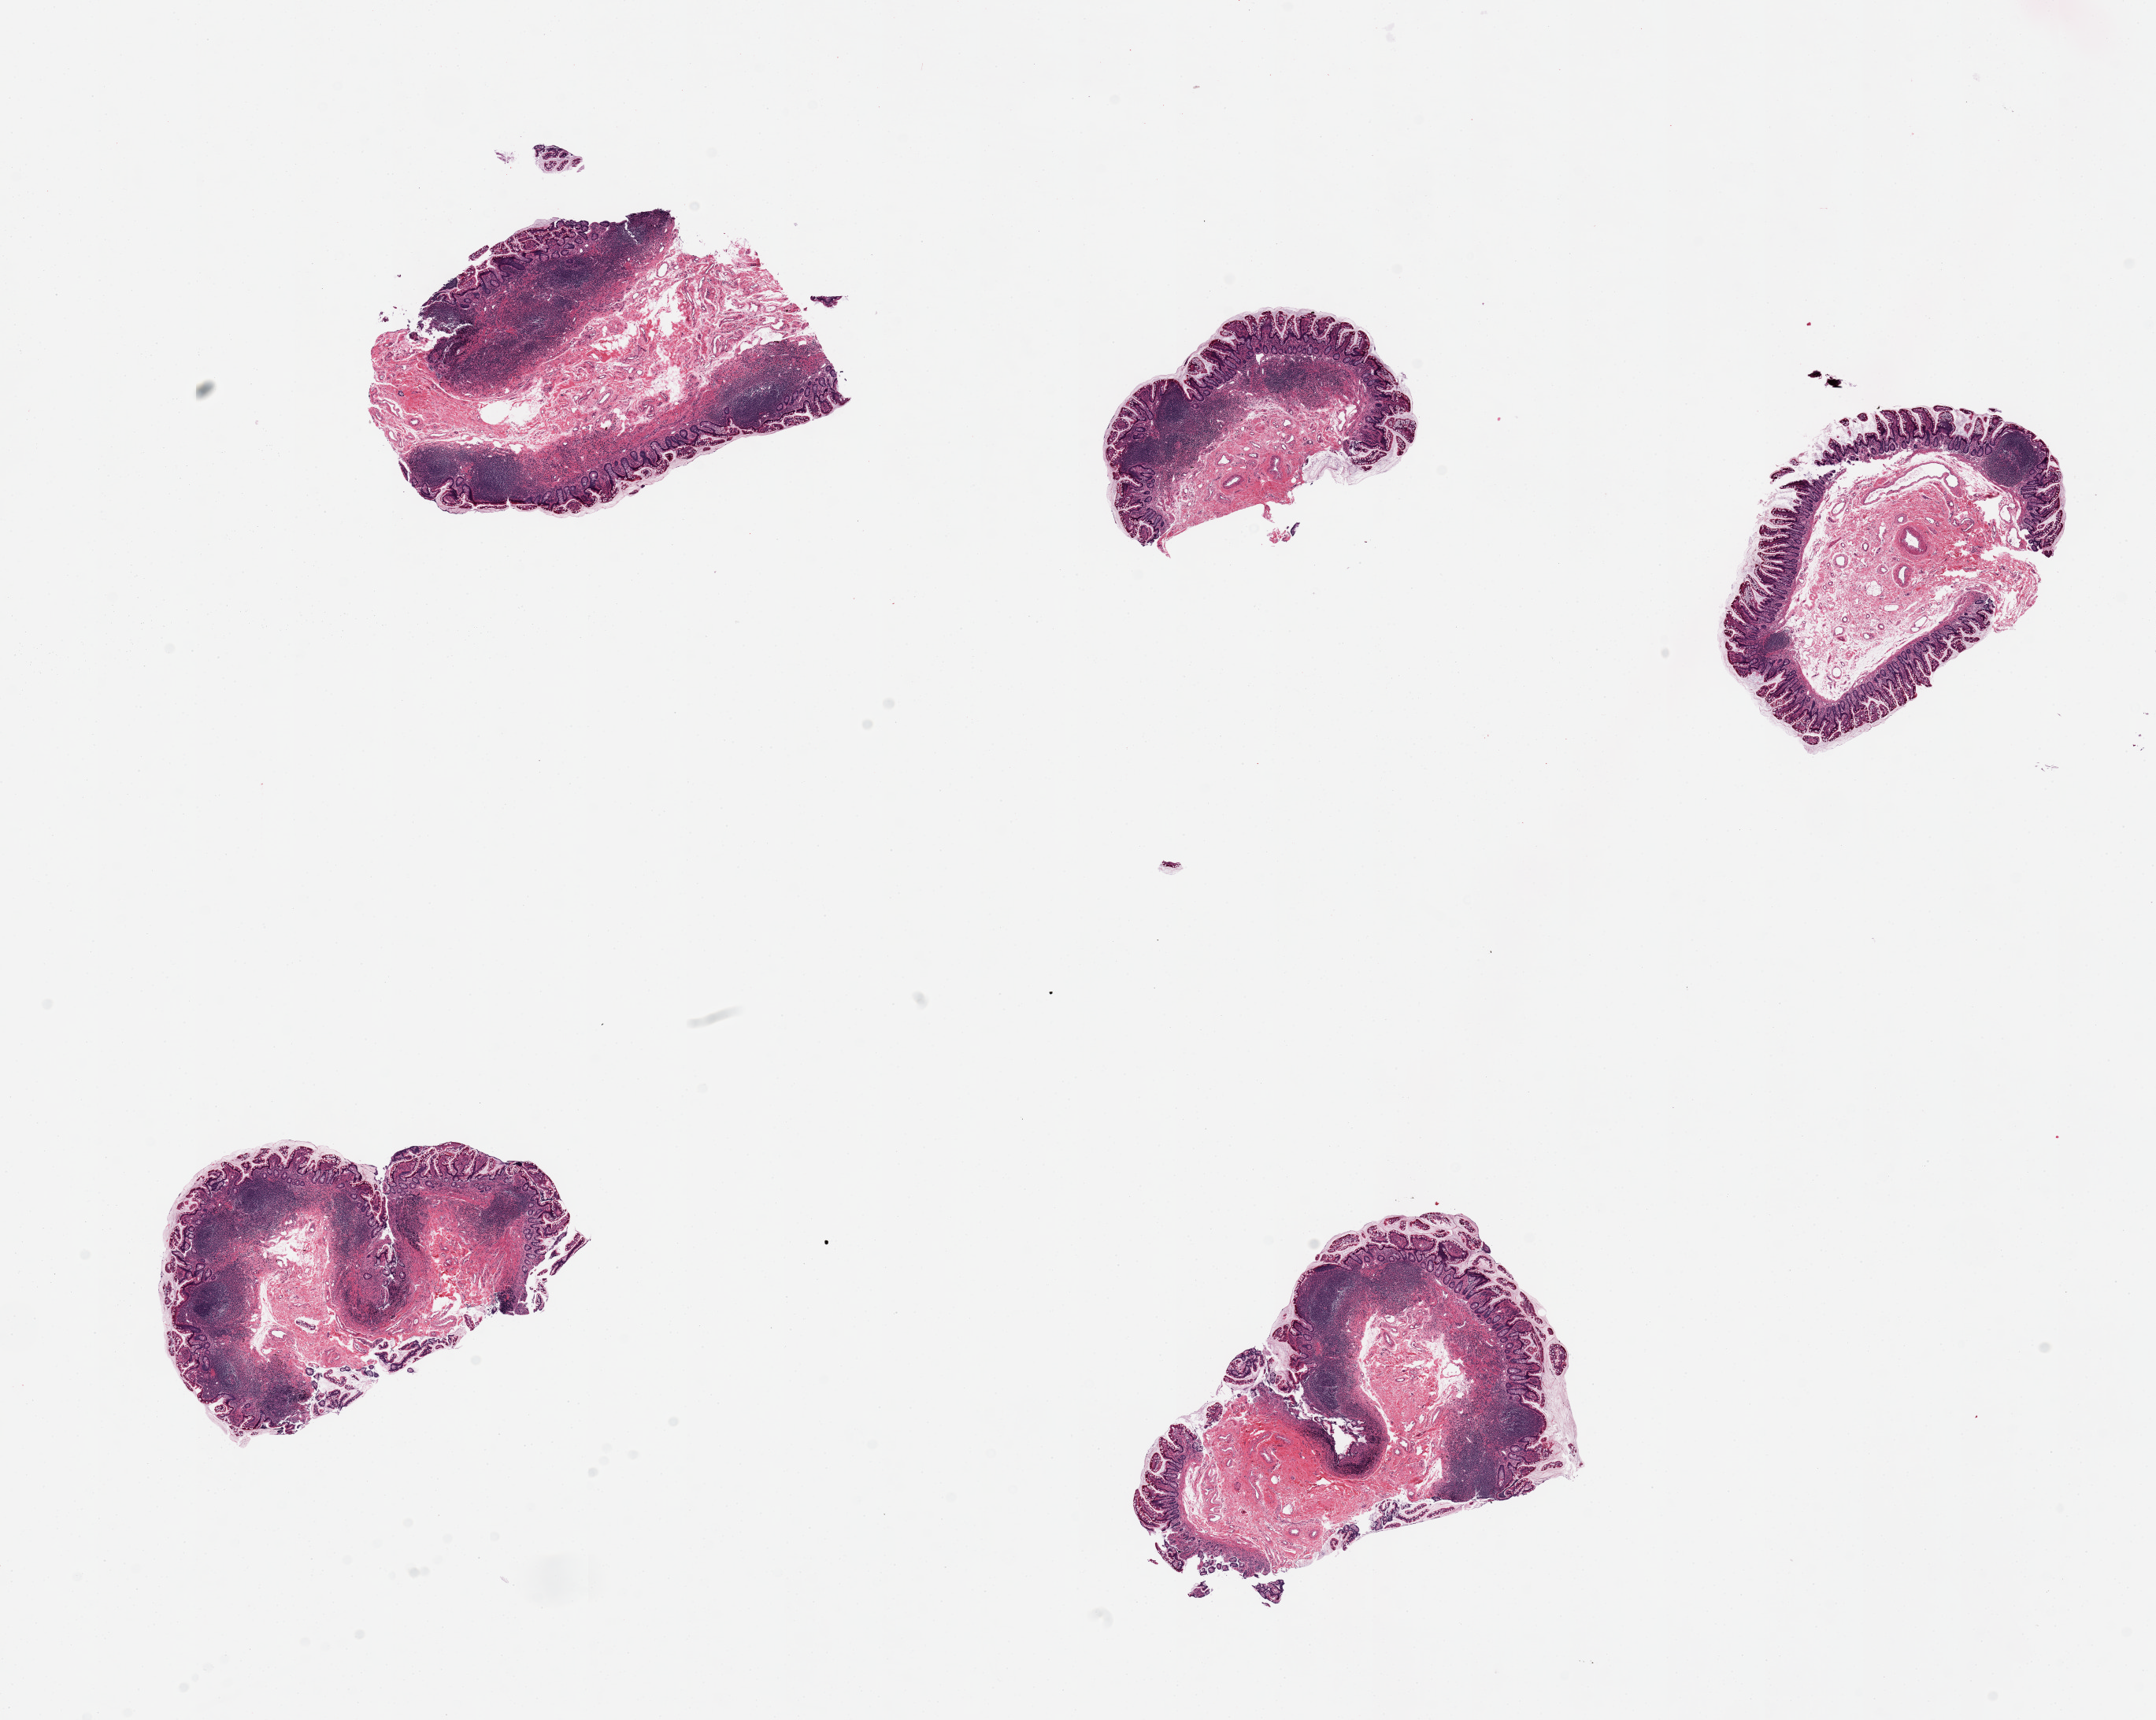
Whole-slide image, haematoxylin and eosin stain — whole scanned area (about 21.7 x 17.3 mm) shown as a low-resolution overview, PAXgene-fixed paraffin-embedded (PFPE) section, section of ileum (target tissue), tissue donor sample. Male donor.
* review note (as recorded): 5 pieces; abundant lymphoid tissue; well dissected, well preserved